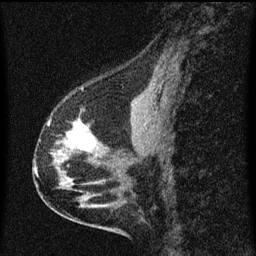
Breast MRI (dynamic contrast-enhanced), one sagittal slice; position 29 of 60 along the scan axis; dynamic contrast-enhanced series, image 2 of 3 at this slice position (ordered by acquisition); 1.5 T; TE 4.2 ms, TR 8 ms; 256 × 256 image matrix, field of view 180 × 180 mm. Female patient, age 56 years.
Structures marked on this image (semi-automatic segmentation, software-assisted and operator-edited):
- analysis volume of interest (the breast-tissue region the enhancement analysis was run in; not a lesion): bounding box (x1, y1, x2, y2) in pixels: (34, 114, 102, 181)
- tumour enhancement mask (voxels above the 70 % enhancement threshold inside the analysis volume of interest): (68, 121, 95, 150)